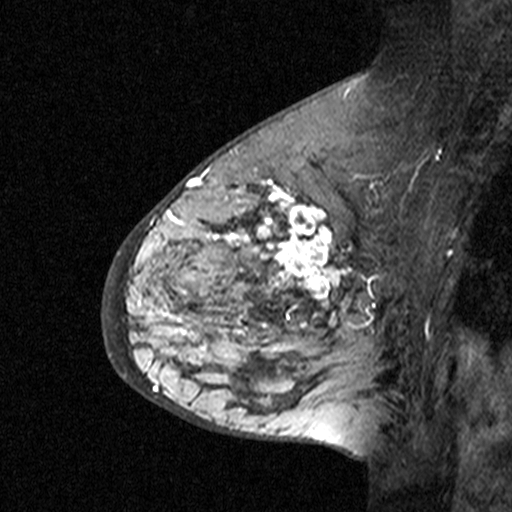
Breast MRI (dynamic contrast-enhanced), one sagittal slice. Position 23 of 44 along the scan axis. Dynamic contrast-enhanced study with each time point stored as its own series, time point 3 of 4 at this slice position (ordered by acquisition time). 1.5 T. TE 4.5 ms, TR 11 ms. 3 mm slice thickness. 512 × 512 image matrix, field of view 200 × 200 mm. Patient: female, 65 years. From the clinical record (not read from this slice): setting: breast cancer imaged before/during neoadjuvant chemotherapy; receptor status: HER2-positive.
Annotated regions visible in this slice (semi-automatic segmentation, software-assisted and operator-edited):
- analysis volume of interest (the breast-tissue region the enhancement analysis was run in; not a lesion): box from (x=182, y=190) to (x=353, y=361) px
- tumour enhancement mask (voxels above the 90 % enhancement threshold inside the analysis volume of interest): (x=186, y=190)–(x=345, y=335)